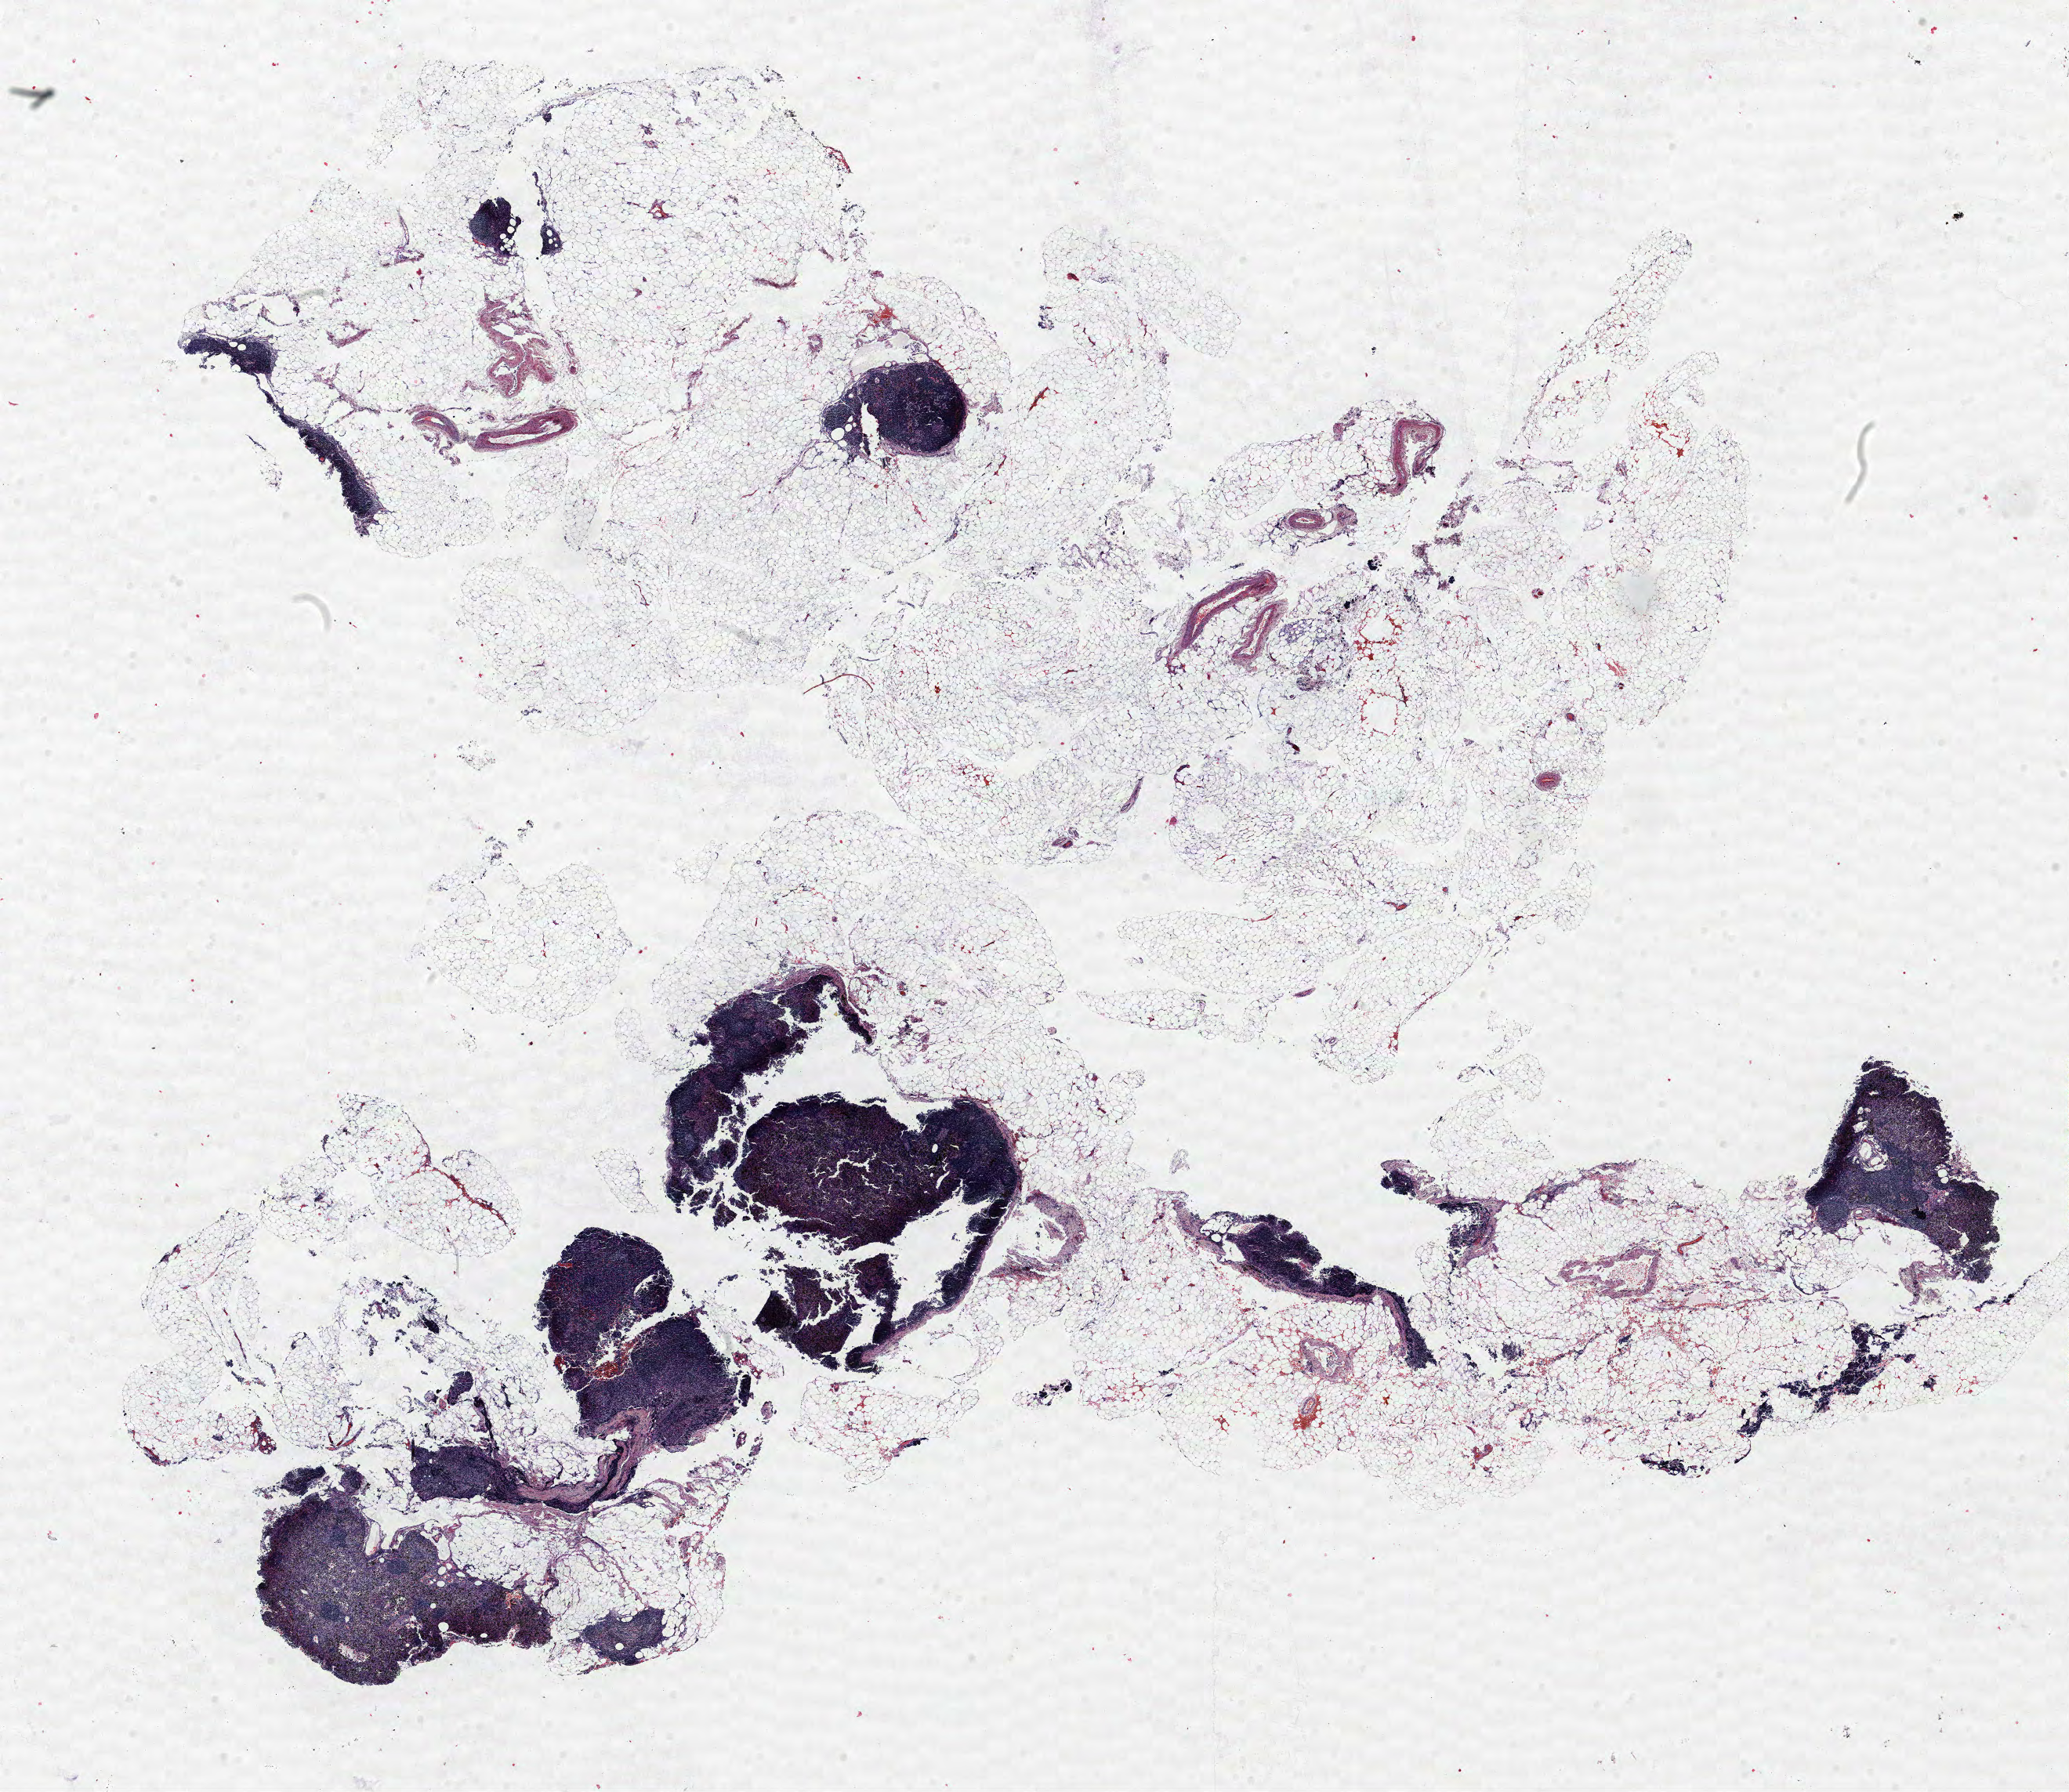
Hematoxylin and eosin (H&E) stained whole-slide image — whole scanned area (about 21.1 x 18.3 mm, slide scanned at 40x) shown as a low-resolution overview; formalin-fixed paraffin-embedded (FFPE) section; lung tissue. Male patient, aged 68 at enrolment. Current smoker at enrolment. Grade: undifferentiated (G4).
Stage (AJCC 6th edition): IIIB. Primary tumour location (clinical record): right upper lobe. Participant's lung-cancer diagnosis: Combined small cell carcinoma. Tumour size (pathology): 30 mm.